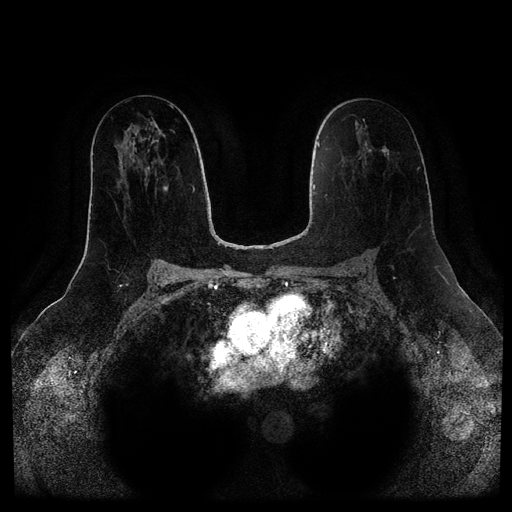
Breast MRI (dynamic contrast-enhanced, multi-phase), one axial slice. Dynamic contrast-enhanced series, time point 2 of 5 at this slice position (early post-contrast). 1.5 T. TE 2.6 ms, TR 5.2 ms. 2 mm slice thickness. 512 × 512 image matrix. Female patient, age 57 years.
Annotated regions visible in this slice (semi-automatic segmentation, software-assisted and operator-edited):
- breast lesion (labelled benign in the annotation): bounding box <382,149,389,155> (left, top, right, bottom; pixels)